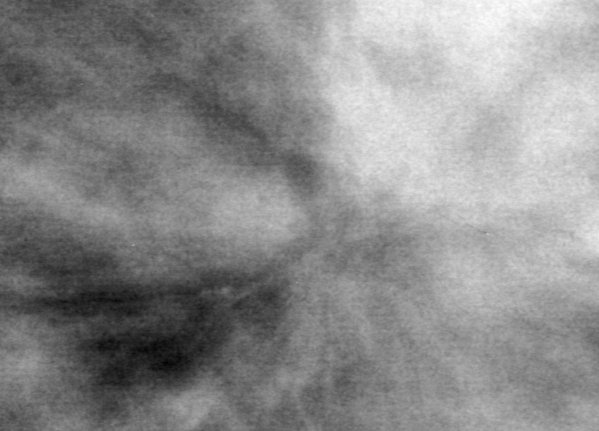
Cropped region of a digitized screen-film mammogram centred on a radiologist-marked abnormality, right breast, CC view.
- Marked abnormality: mass, shape architectural distortion, margins spiculated; BI-RADS assessment category 5; subtlety rating 3 on a 1 (subtle) to 5 (obvious) scale; pathology result (as recorded, not read from the image): malignant.